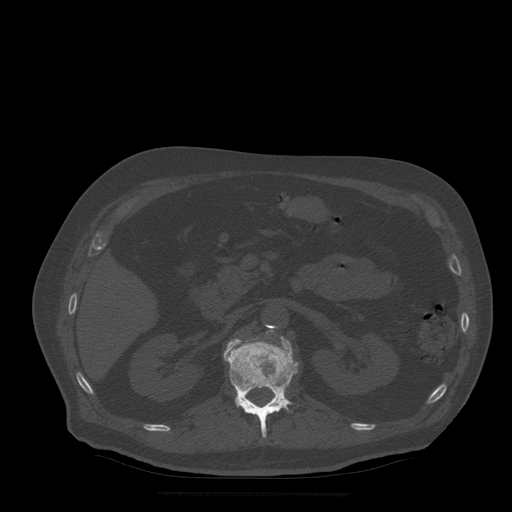
CT including the spine, one axial slice. Slice 193 of 522 in the series (ordered by position). Bone window (W 1800 / L 400 HU). 1.25 mm slice thickness. 512 × 512 image matrix, field of view 420 × 420 mm. Patient age 72 years. From the clinical record (not read from this slice): primary cancer: prostate.
Structures marked on this image (semi-automatic segmentation, software-assisted and operator-edited):
- L1 vertebra: bounding box <224,337,299,438> (left, top, right, bottom; pixels)
- L2 vertebra: <267,330,274,333>